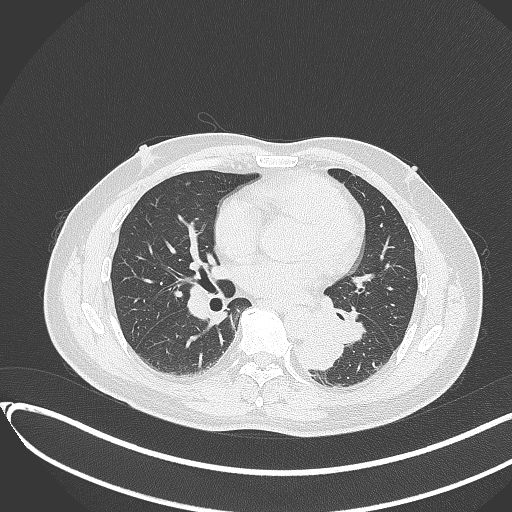
Chest CT, one axial slice; slice 160 of 417 in the series (ordered by position); 120 kVp; lung window (W 1500 / L -600 HU); 1 mm slice thickness; 512 × 512 image matrix, field of view 400 × 400 mm. Male patient, age 54 years. Case-level facts recorded for this patient, not image findings: clinical TNM (as recorded): T3 N0 M0.
Structures marked on this image (bounding box drawn by a radiologist):
- lung tumour (recorded histology: squamous cell carcinoma): bounding box <291,328,346,375> (left, top, right, bottom; pixels)